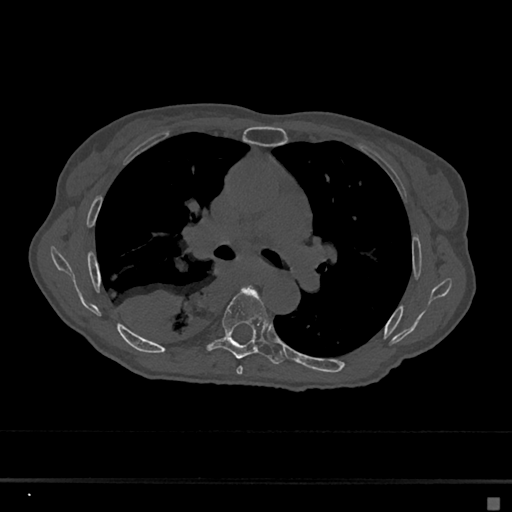
CT including the spine, one axial slice; position 424 of 797 along the scan axis; reconstruction kernel Br40s/3; 120 kVp; bone window (W 1800 / L 400 HU); 0.5 mm slice thickness; 512 × 512 image matrix. Female patient, age 68 years. Case-level facts recorded for this patient, not image findings: primary cancer: renal.
Structures marked on this image (semi-automatically segmented with operator editing):
- T5 vertebra: bounding box (x1, y1, x2, y2) in pixels: (236, 286, 259, 375)
- T6 vertebra: (207, 286, 284, 364)